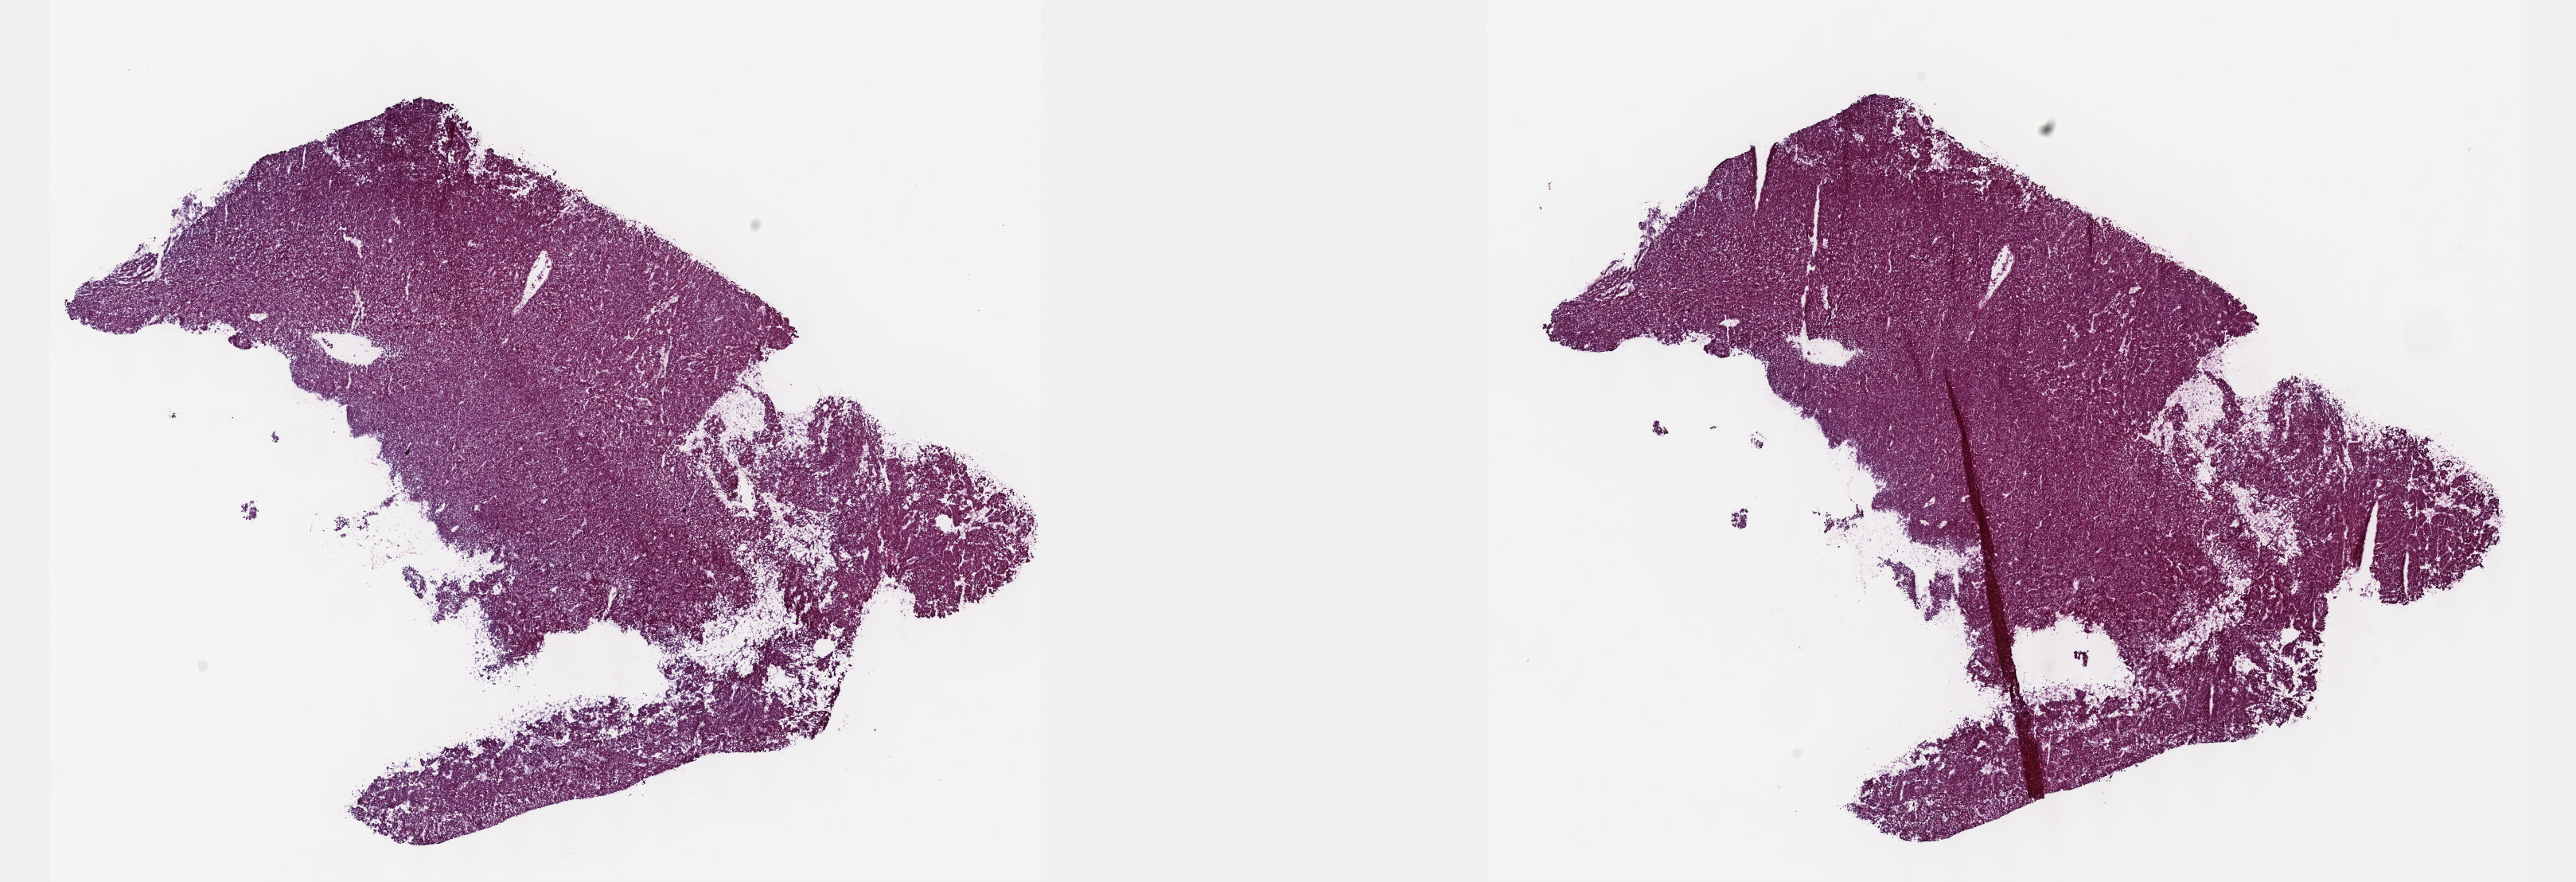
Whole-slide histology image, H&E-stained, low-resolution overview of the scanned area, about 26.2 x 9.0 mm, frozen section from the top of the tissue portion, liver, primary tumour sample. Patient: male, age at initial diagnosis 61 years. Histologic grade: G1 (well differentiated). Slide review estimates, as recorded: tumour cells 100%, tumour nuclei 80%, normal cells 0%, stromal cells 0%, necrosis 0%. Infiltration values recorded for this section: lymphocyte infiltration 2%, monocyte infiltration 0%, neutrophil infiltration 0%.
Diagnosis: Hepatocellular carcinoma, NOS. AJCC pathologic stage: IIIA (6th edition).